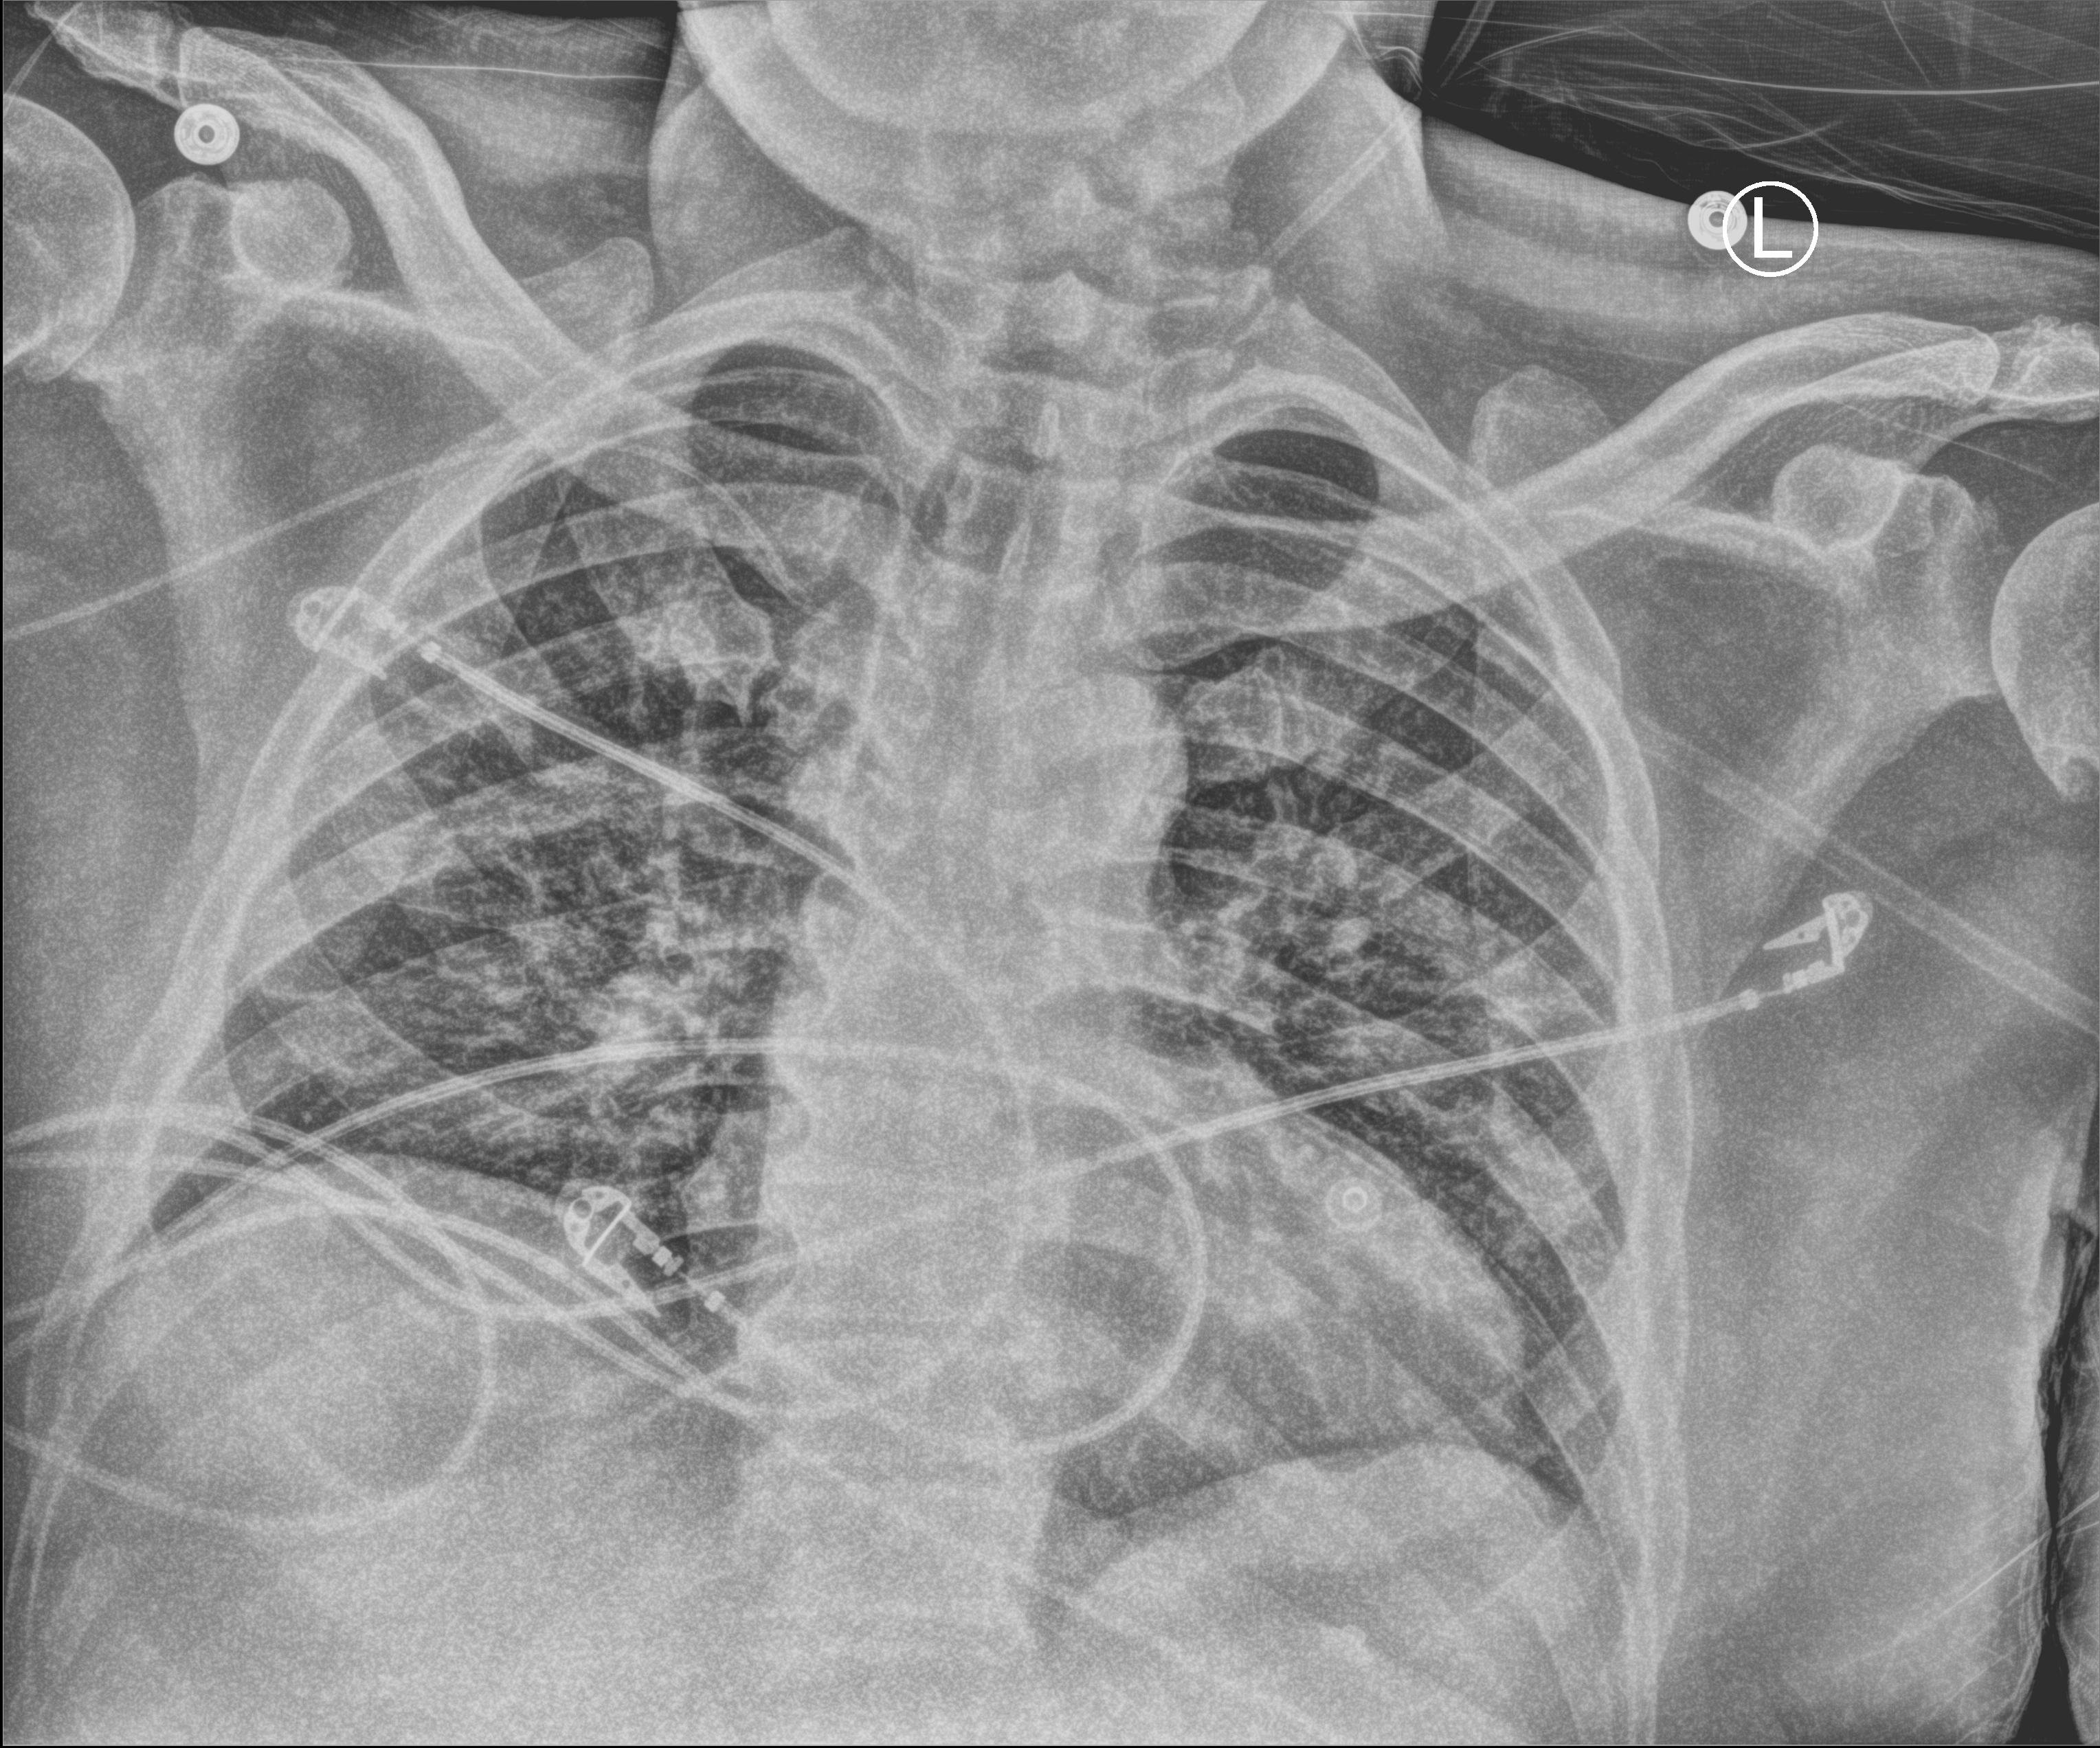
Bedside chest radiograph (computed radiography); anteroposterior (AP) projection. Male patient hospitalised with COVID-19, age 18–59 years.
From the hospital-stay record, not from the radiograph (when in the stay this image was taken is not recorded): admitted to intensive care during this hospital stay: yes; mechanically ventilated during this hospital stay: yes; diabetes (admission record): no.